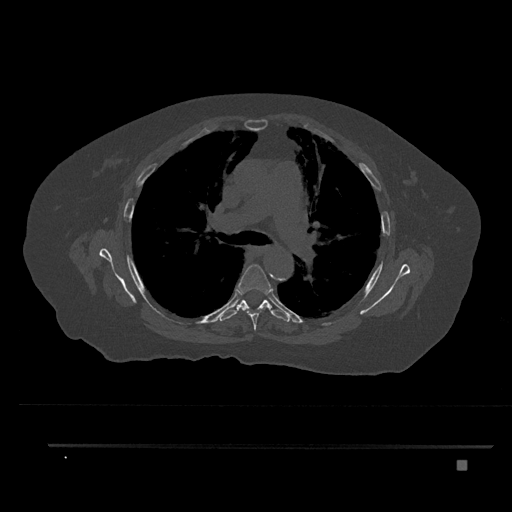
CT including the spine, one axial slice. Position 549 of 797 along the scan axis. Reconstruction kernel Br40s/3. 120 kVp. Bone window (W 1800 / L 400 HU). 512 × 512 image matrix, field of view 437 × 437 mm. Patient: female, 76 years. From the clinical record (not read from this slice): primary cancer: lung; vertebrae with lytic lesions (as recorded): T11, L3.
Outlined on this slice (semi-automatically segmented with operator editing):
- T5 vertebra: bounding box (x1, y1, x2, y2) in pixels: (238, 264, 271, 330)
- T6 vertebra: (219, 300, 290, 322)